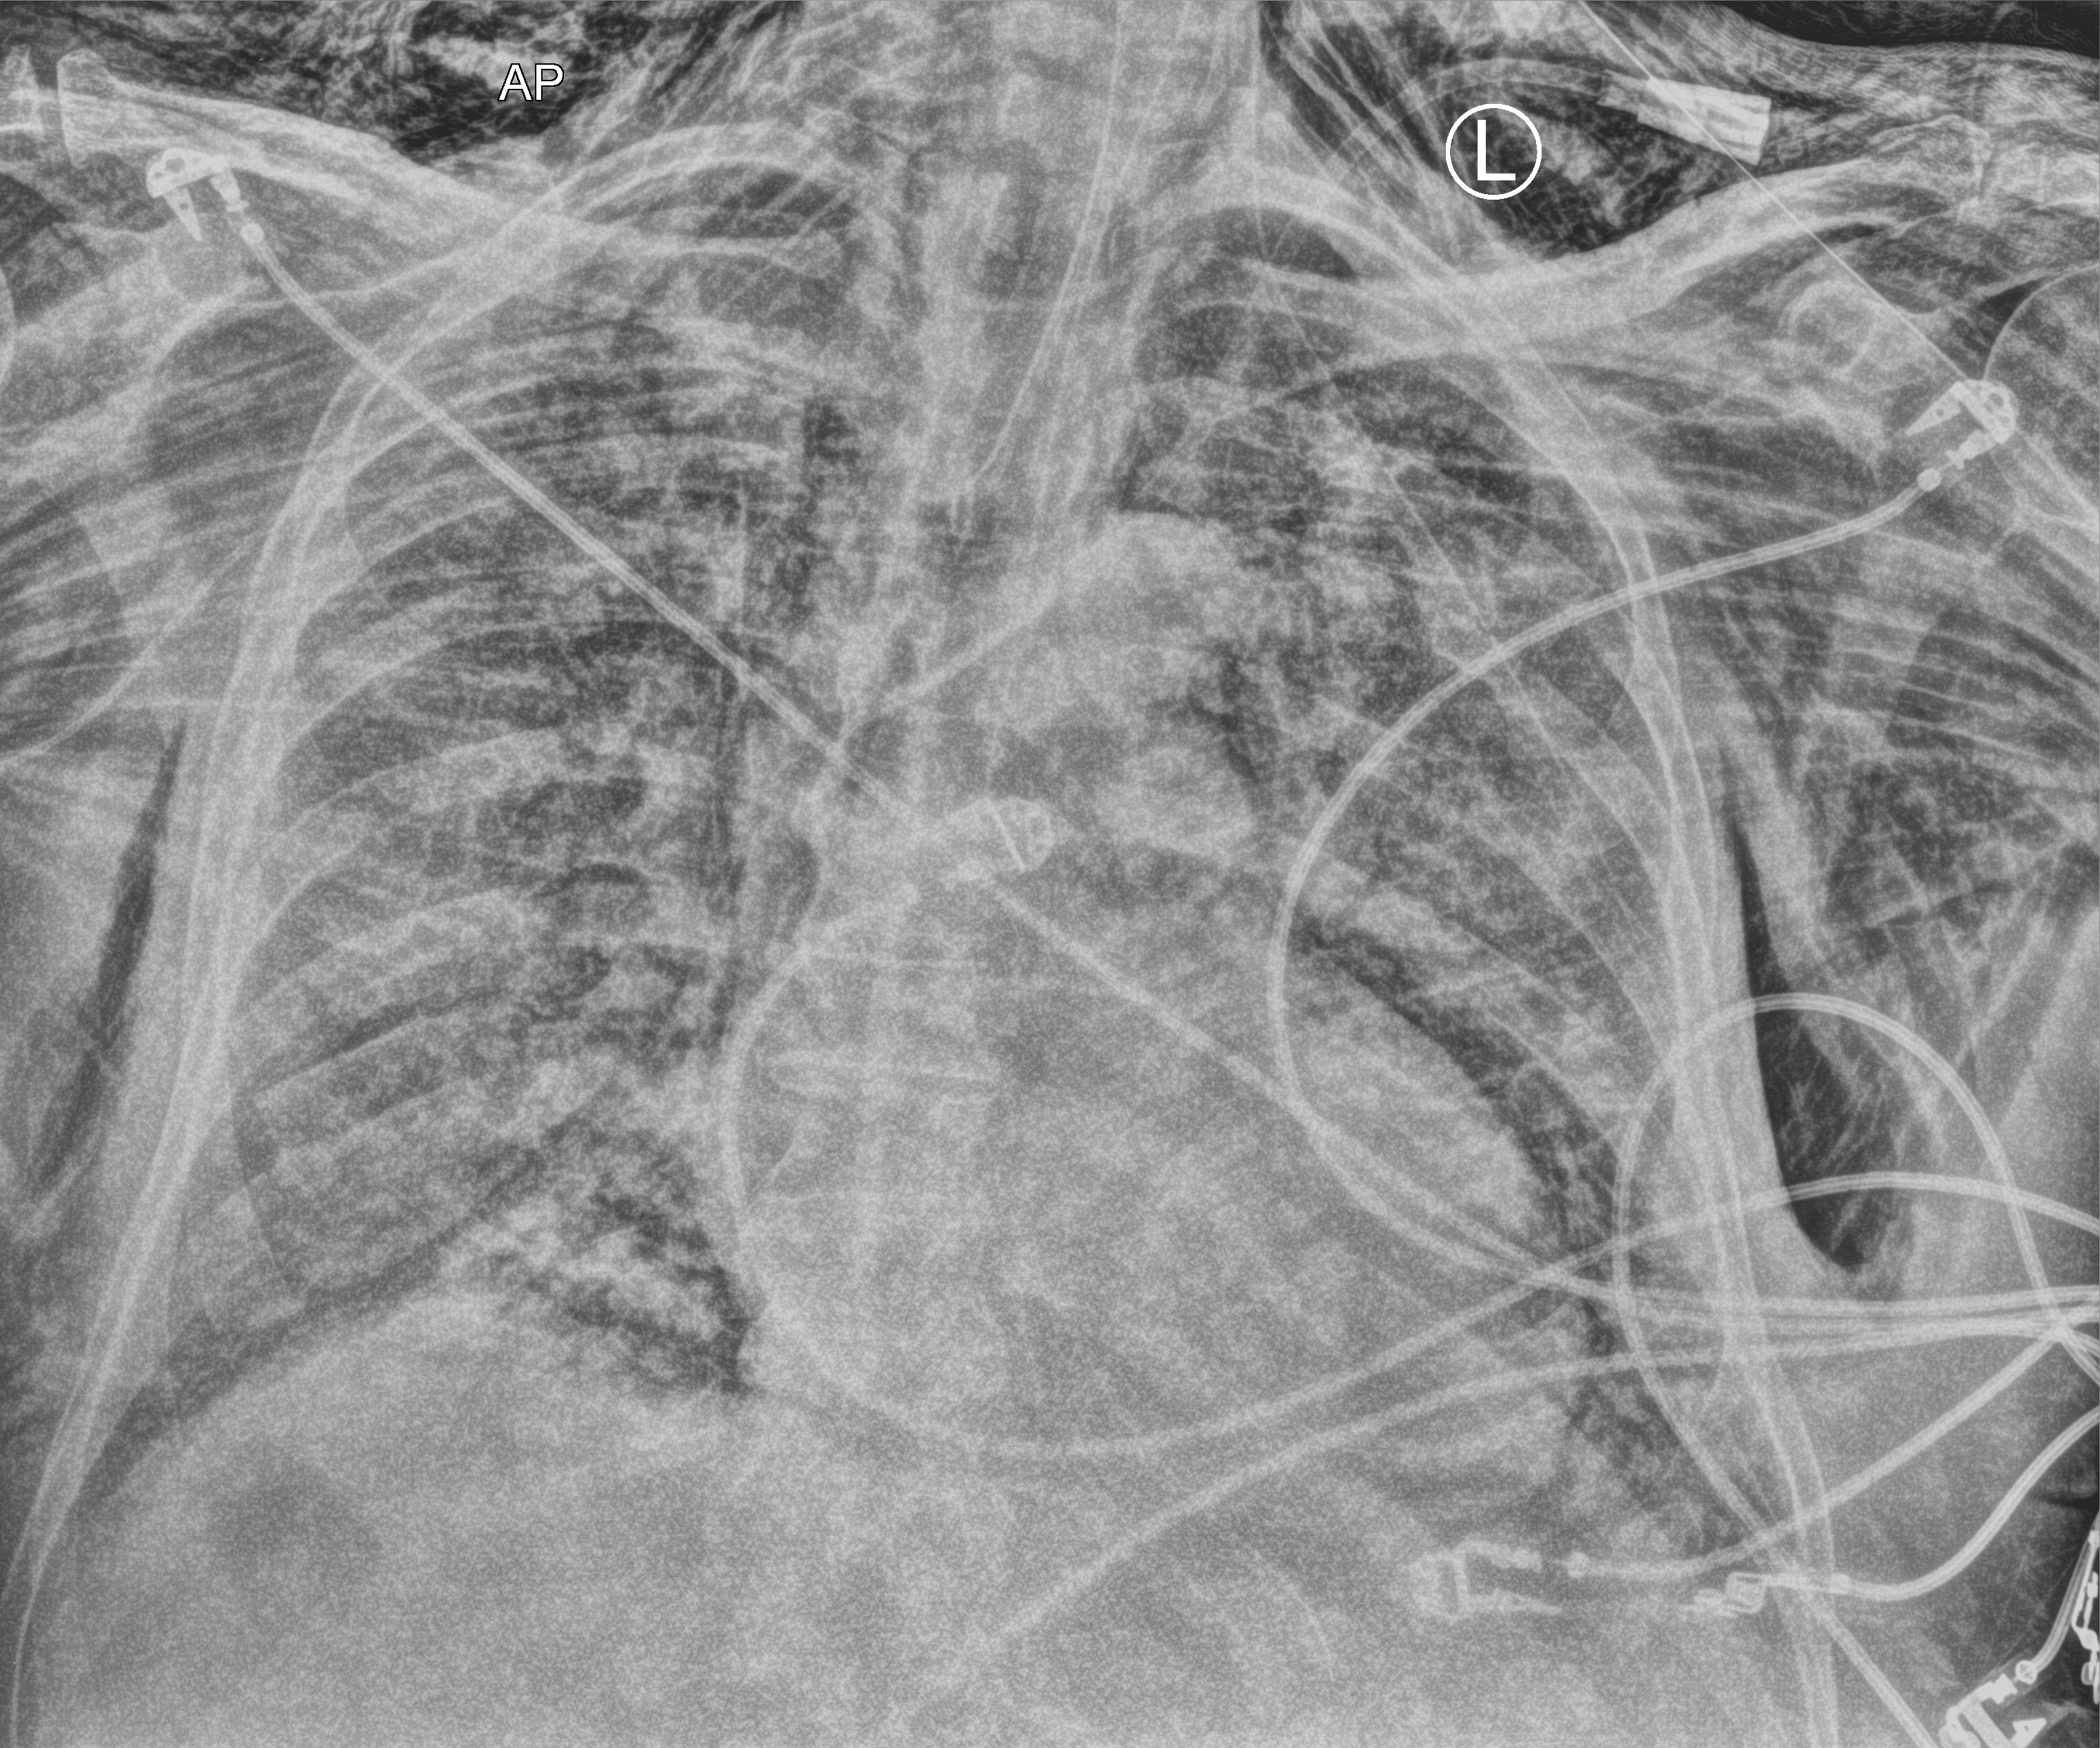
Bedside chest radiograph (computed radiography); anteroposterior (AP) projection. Male patient hospitalised with COVID-19, age 75–90 years.
From the hospital-stay record, not from the radiograph (when in the stay this image was taken is not recorded):
- mechanically ventilated during this hospital stay: yes
- other chronic lung disease (admission record): no